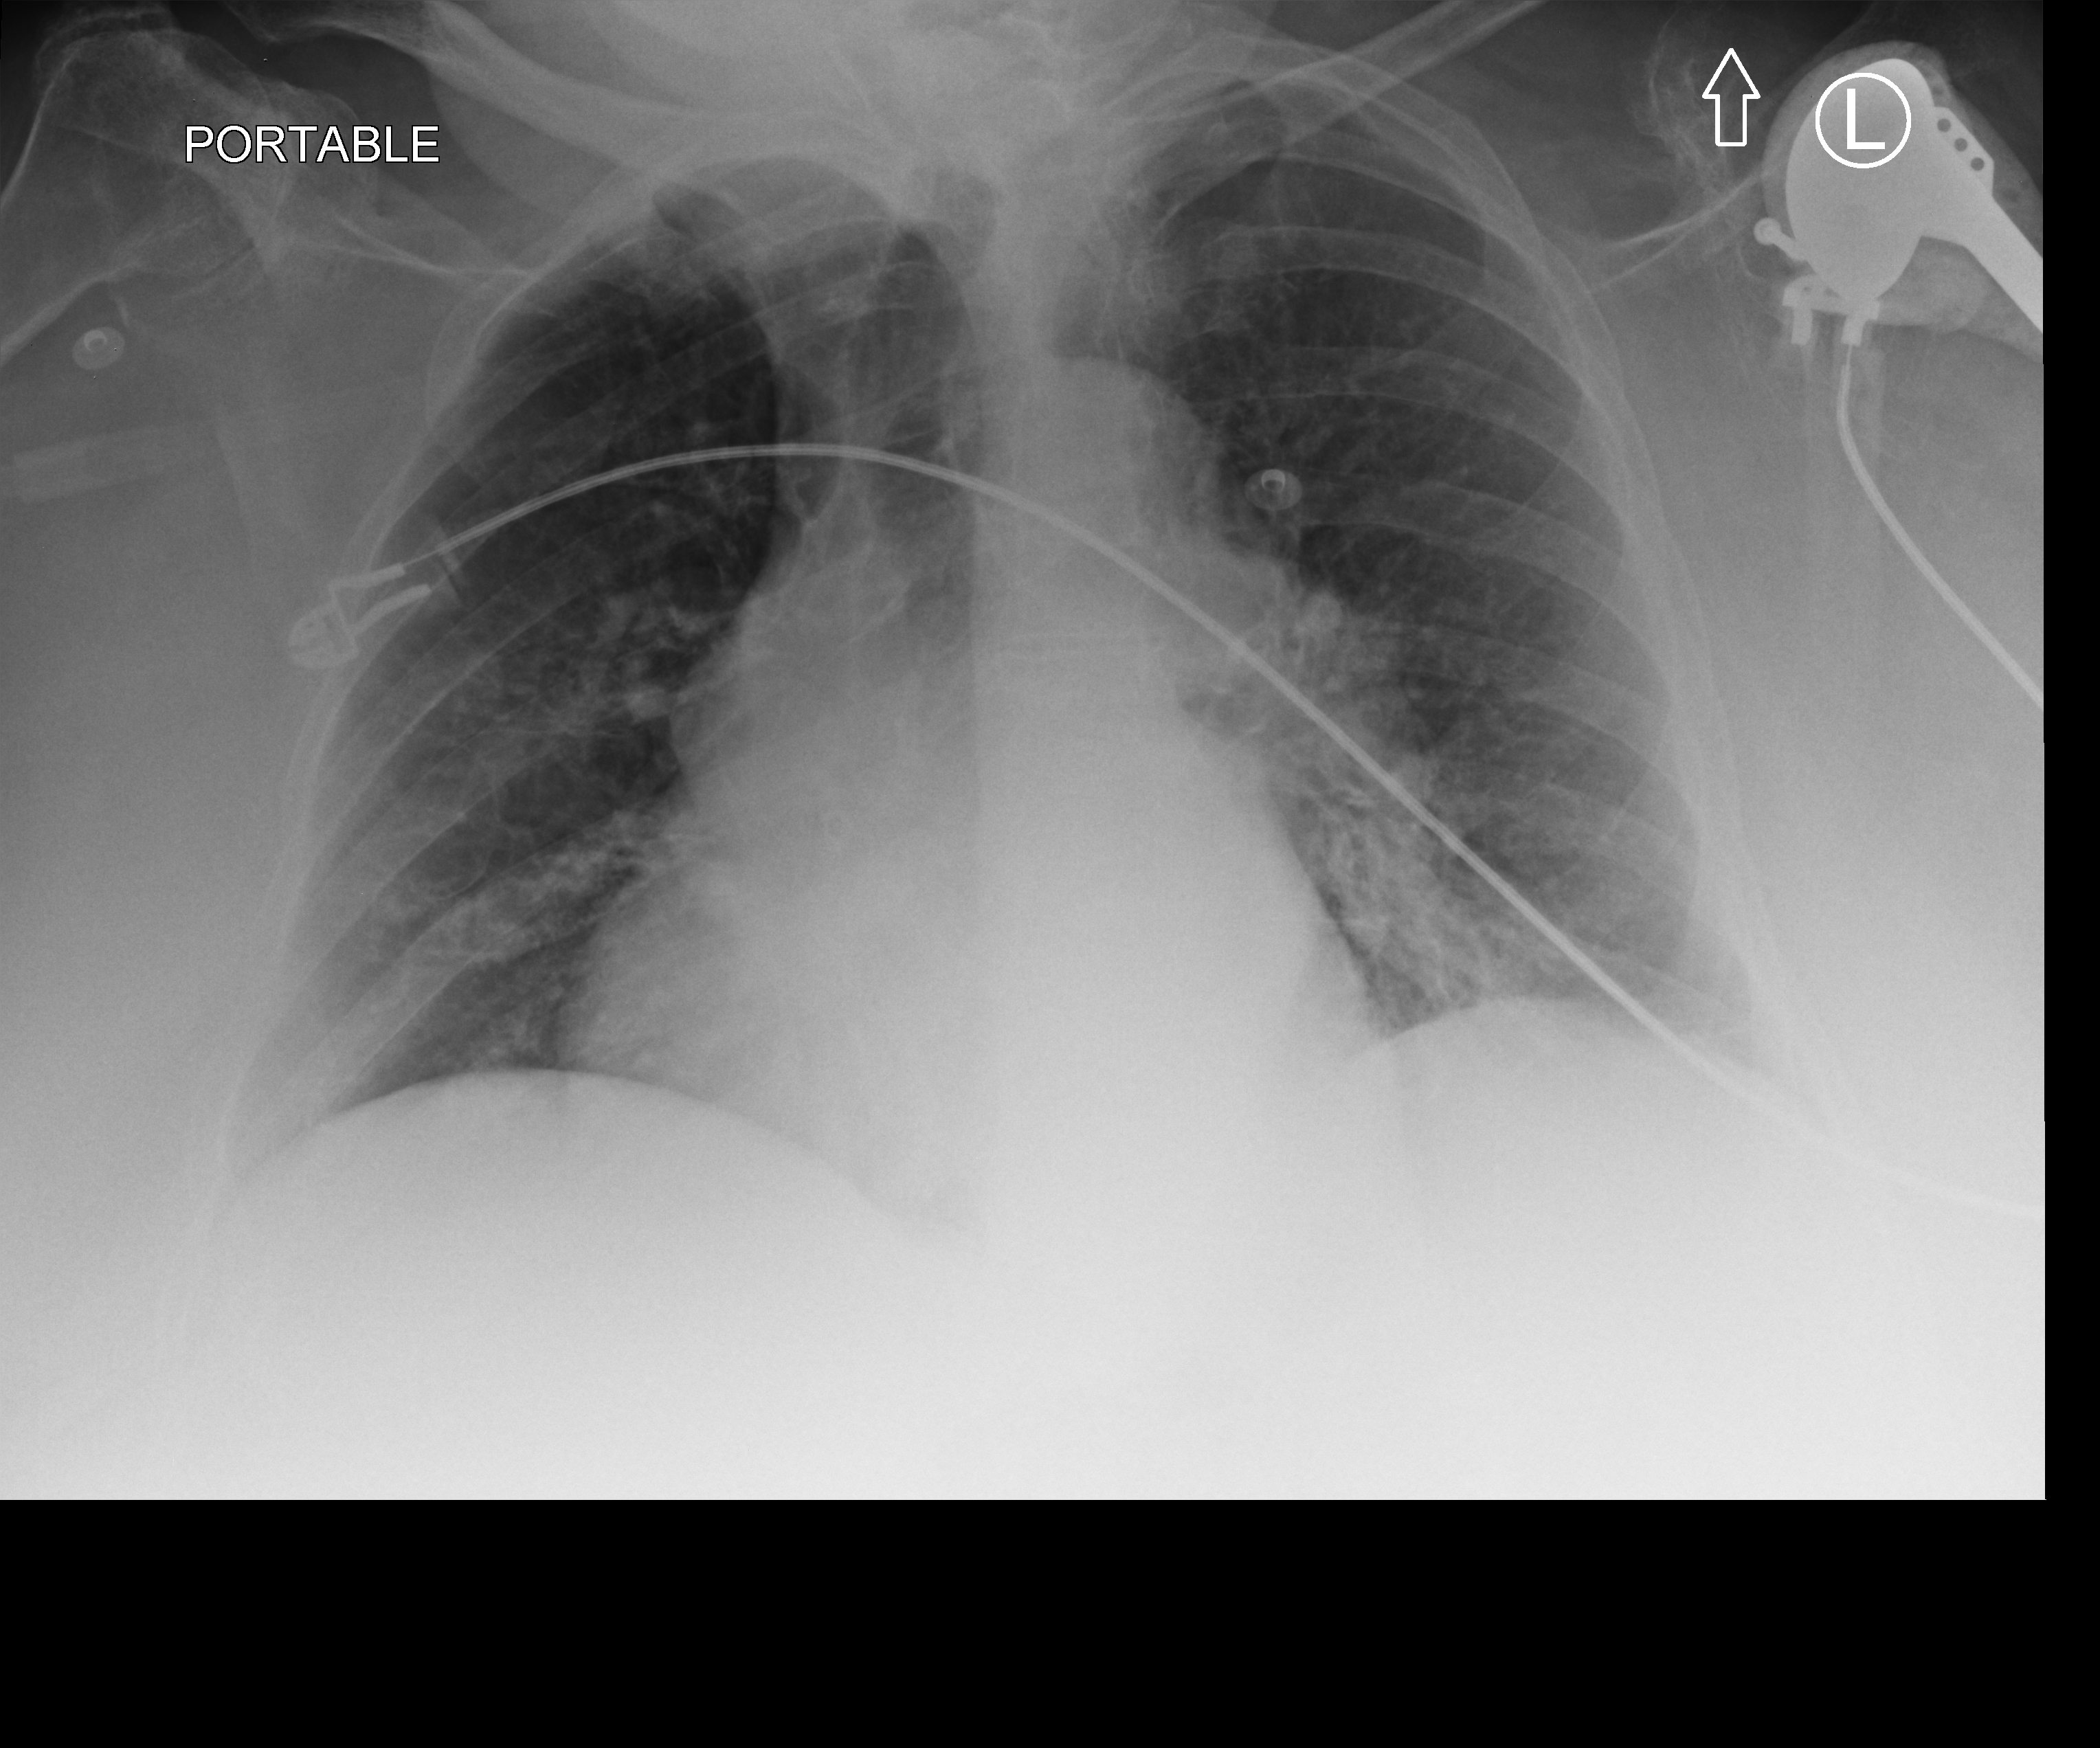
Chest X-ray (portable), anteroposterior (AP) projection. Female patient hospitalised with COVID-19, age 75–90 years.
Admission-level facts for this patient (not findings on this image; timing relative to this image not recorded):
- mechanically ventilated during this hospital stay: no